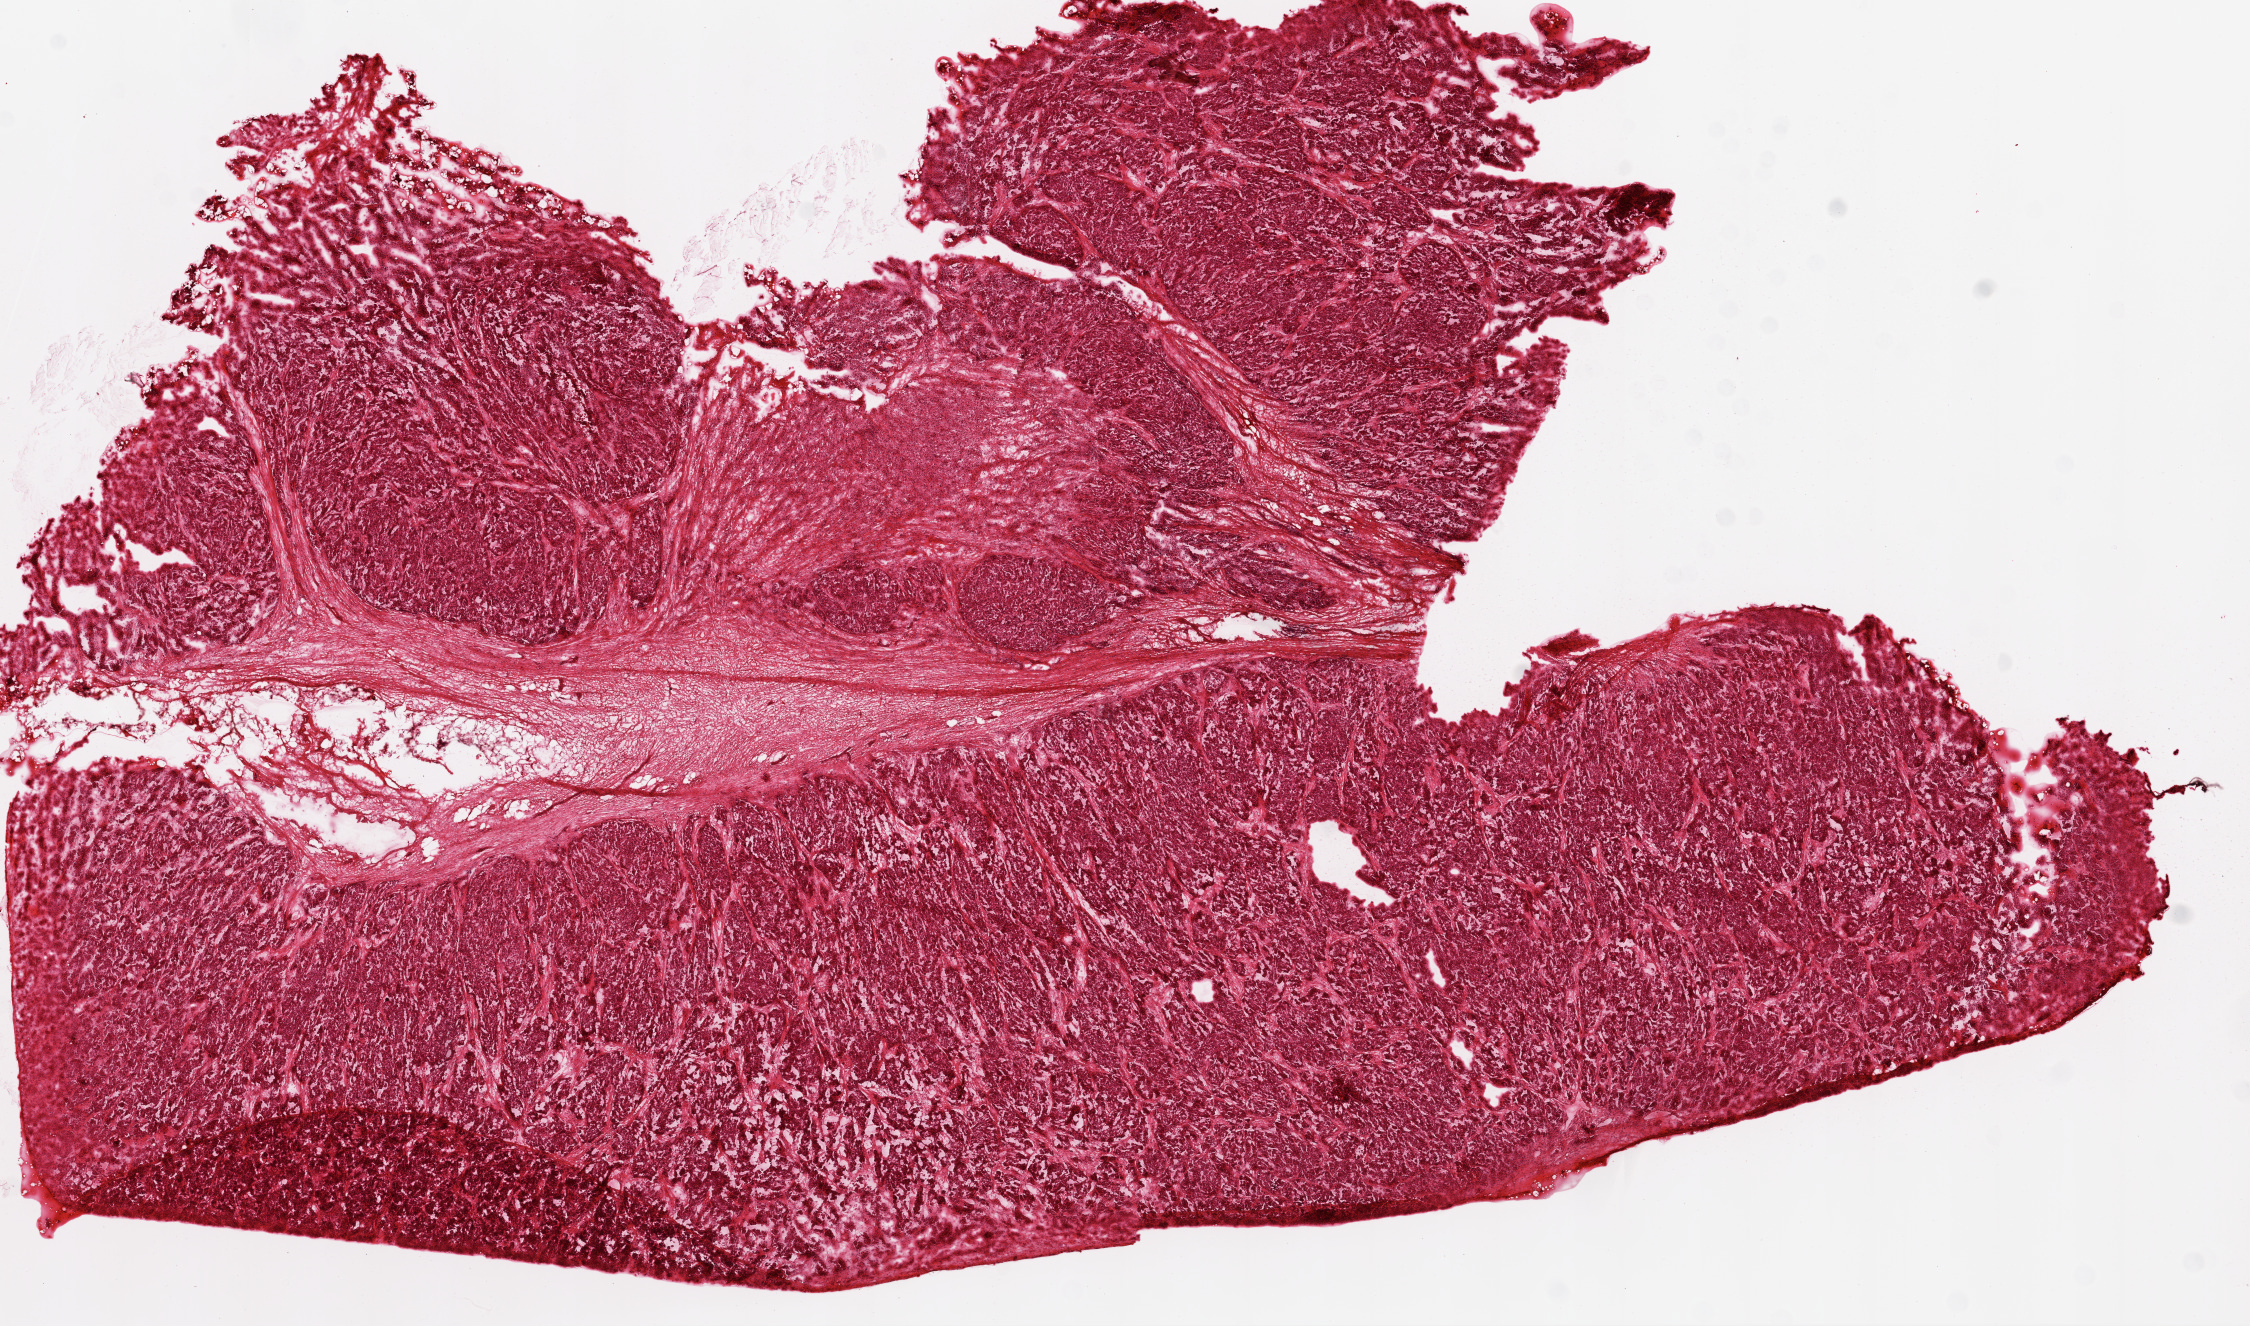
H&E-stained whole-slide image — a low-resolution overview of the entire scanned area, about 18.1 x 10.6 mm (slide scanned at 20x). Frozen section from the top of the tissue portion. Primary tumour sample from the ovary. Patient: female, age at initial diagnosis 67 years. Histologic grade: G3 (poorly differentiated). Composition of this section per pathologist review: tumour cells 90%, tumour nuclei 90%, normal cells 0%, stromal cells 10%, necrosis 0%.
* FIGO stage: IIIC
* diagnosis: Serous cystadenocarcinoma, NOS
* laterality: bilateral